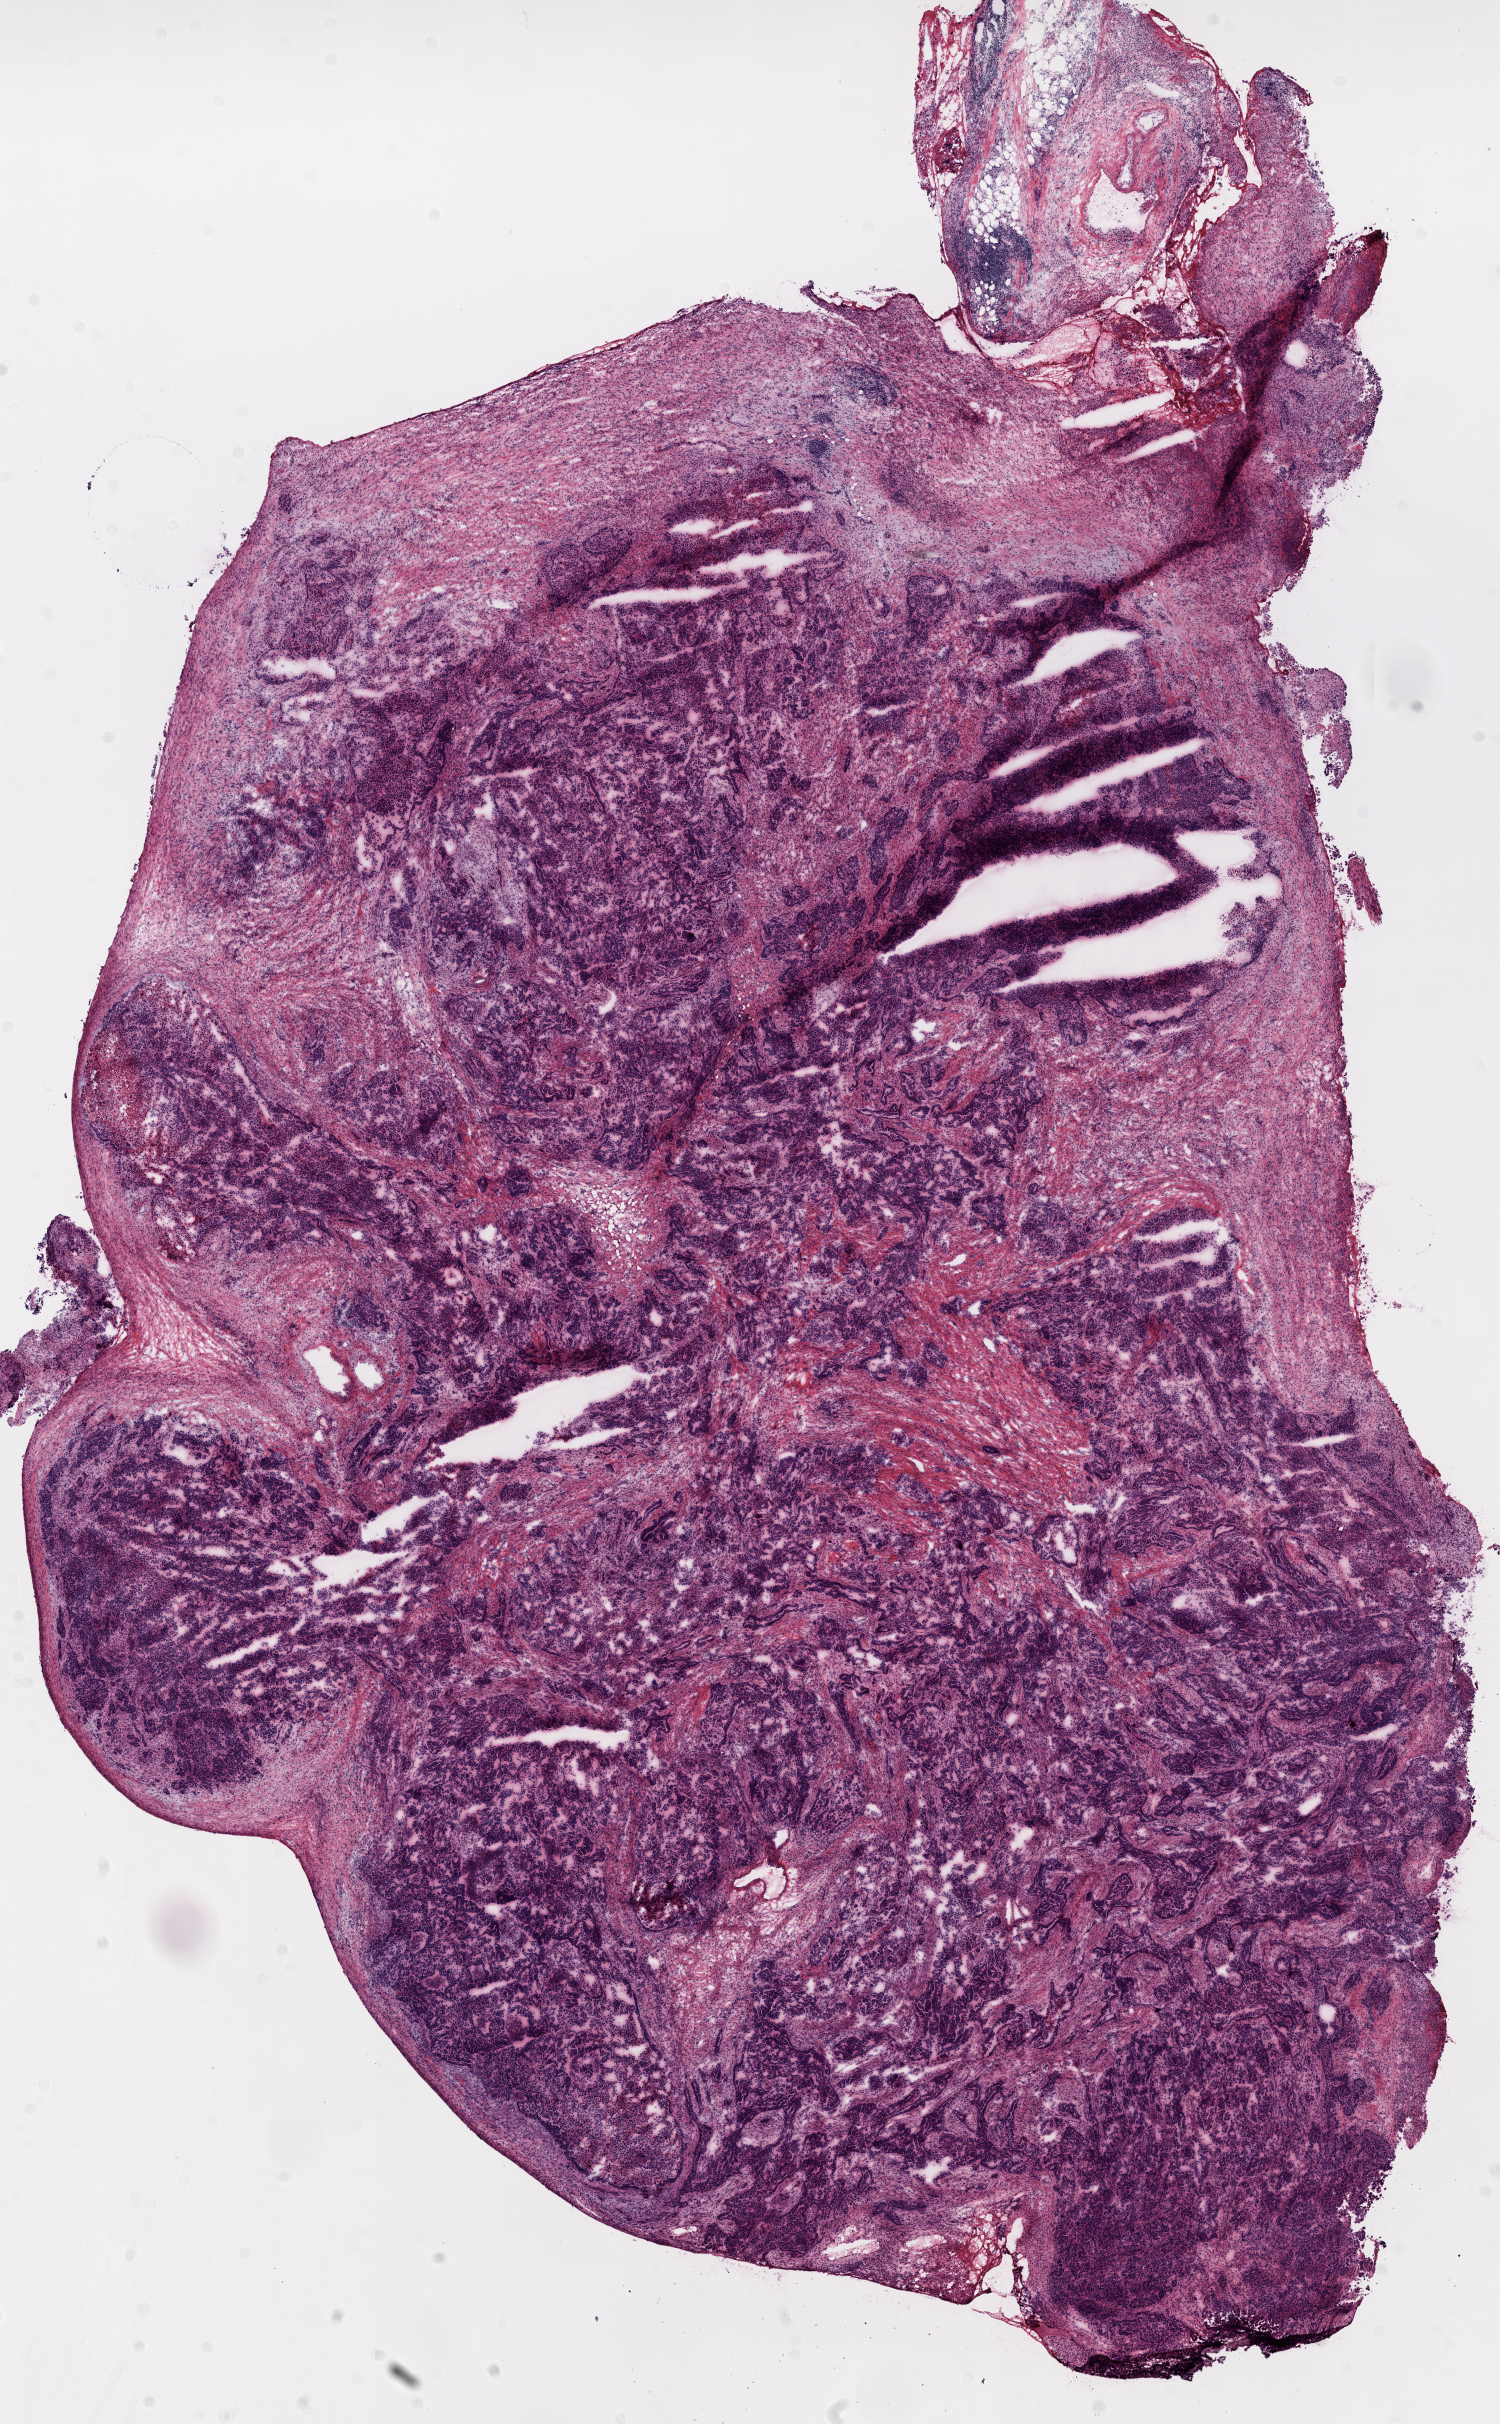
Whole-slide histology image, H&E — a low-resolution overview of the entire scanned area, about 12.0 x 19.5 mm (acquisition: 20x scan); frozen section from the top of the tissue portion; ovary, primary tumour sample. Female, age 59 years at initial diagnosis. Histologic grade: G3 (poorly differentiated). Pathologist review of this section (percent, as recorded): tumour cells 80%, tumour nuclei 80%, normal cells 0%, stromal cells 20%, necrosis 0%.
FIGO stage: IIIC. Diagnosis: Serous cystadenocarcinoma, NOS.